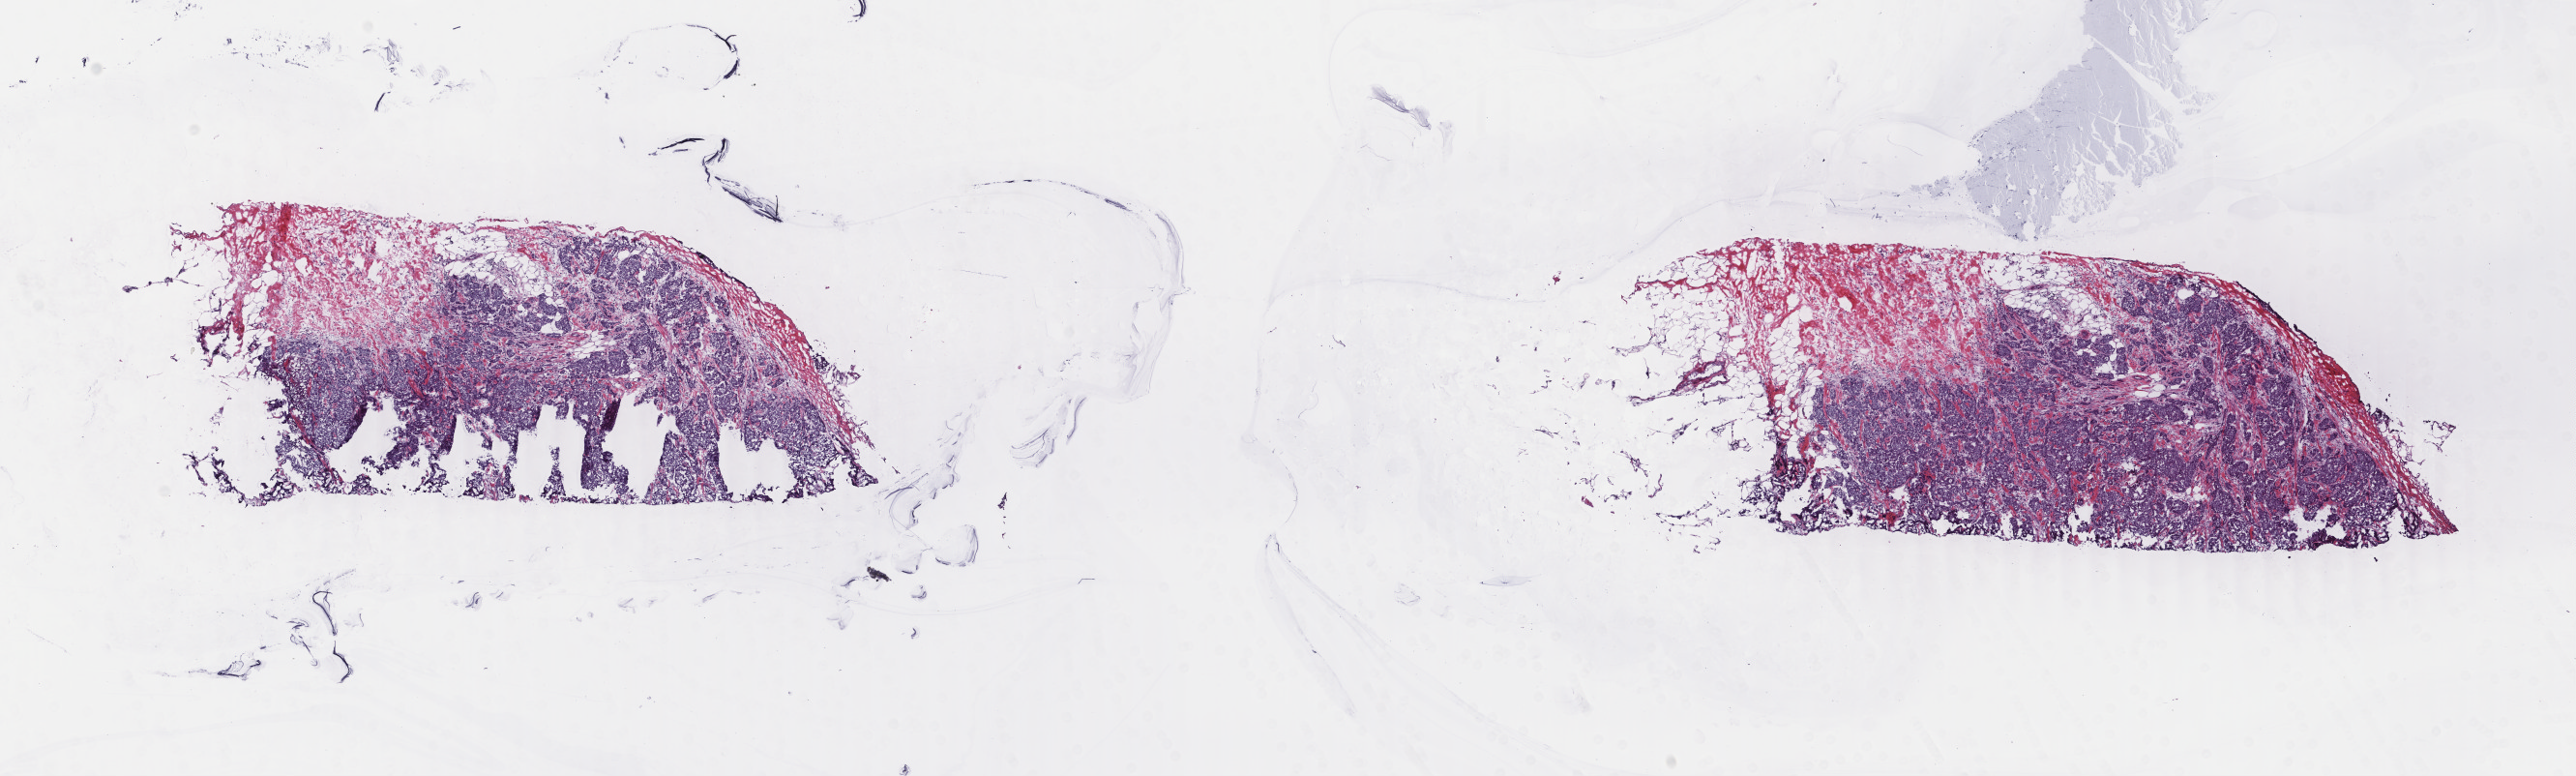
Whole-slide histology image, H&E — low-resolution overview of the scanned area, about 21.2 x 6.4 mm (acquisition: 40x scan). Frozen section from the top of the tissue portion. Breast, primary tumour sample. Patient: male, age at initial diagnosis 68 years. Slide review estimates, as recorded: tumour cells 60%, tumour nuclei 60%, normal cells 0%, stromal cells 30%, necrosis 10%. Inflammatory infiltration, as recorded: lymphocyte infiltration 40%, monocyte infiltration 20%, neutrophil infiltration 20%.
* AJCC pathologic stage: IIB (6th edition)
* diagnosis: Infiltrating duct carcinoma, NOS
* lymph nodes positive (case pathology): 1 of 25 examined
* laterality: left